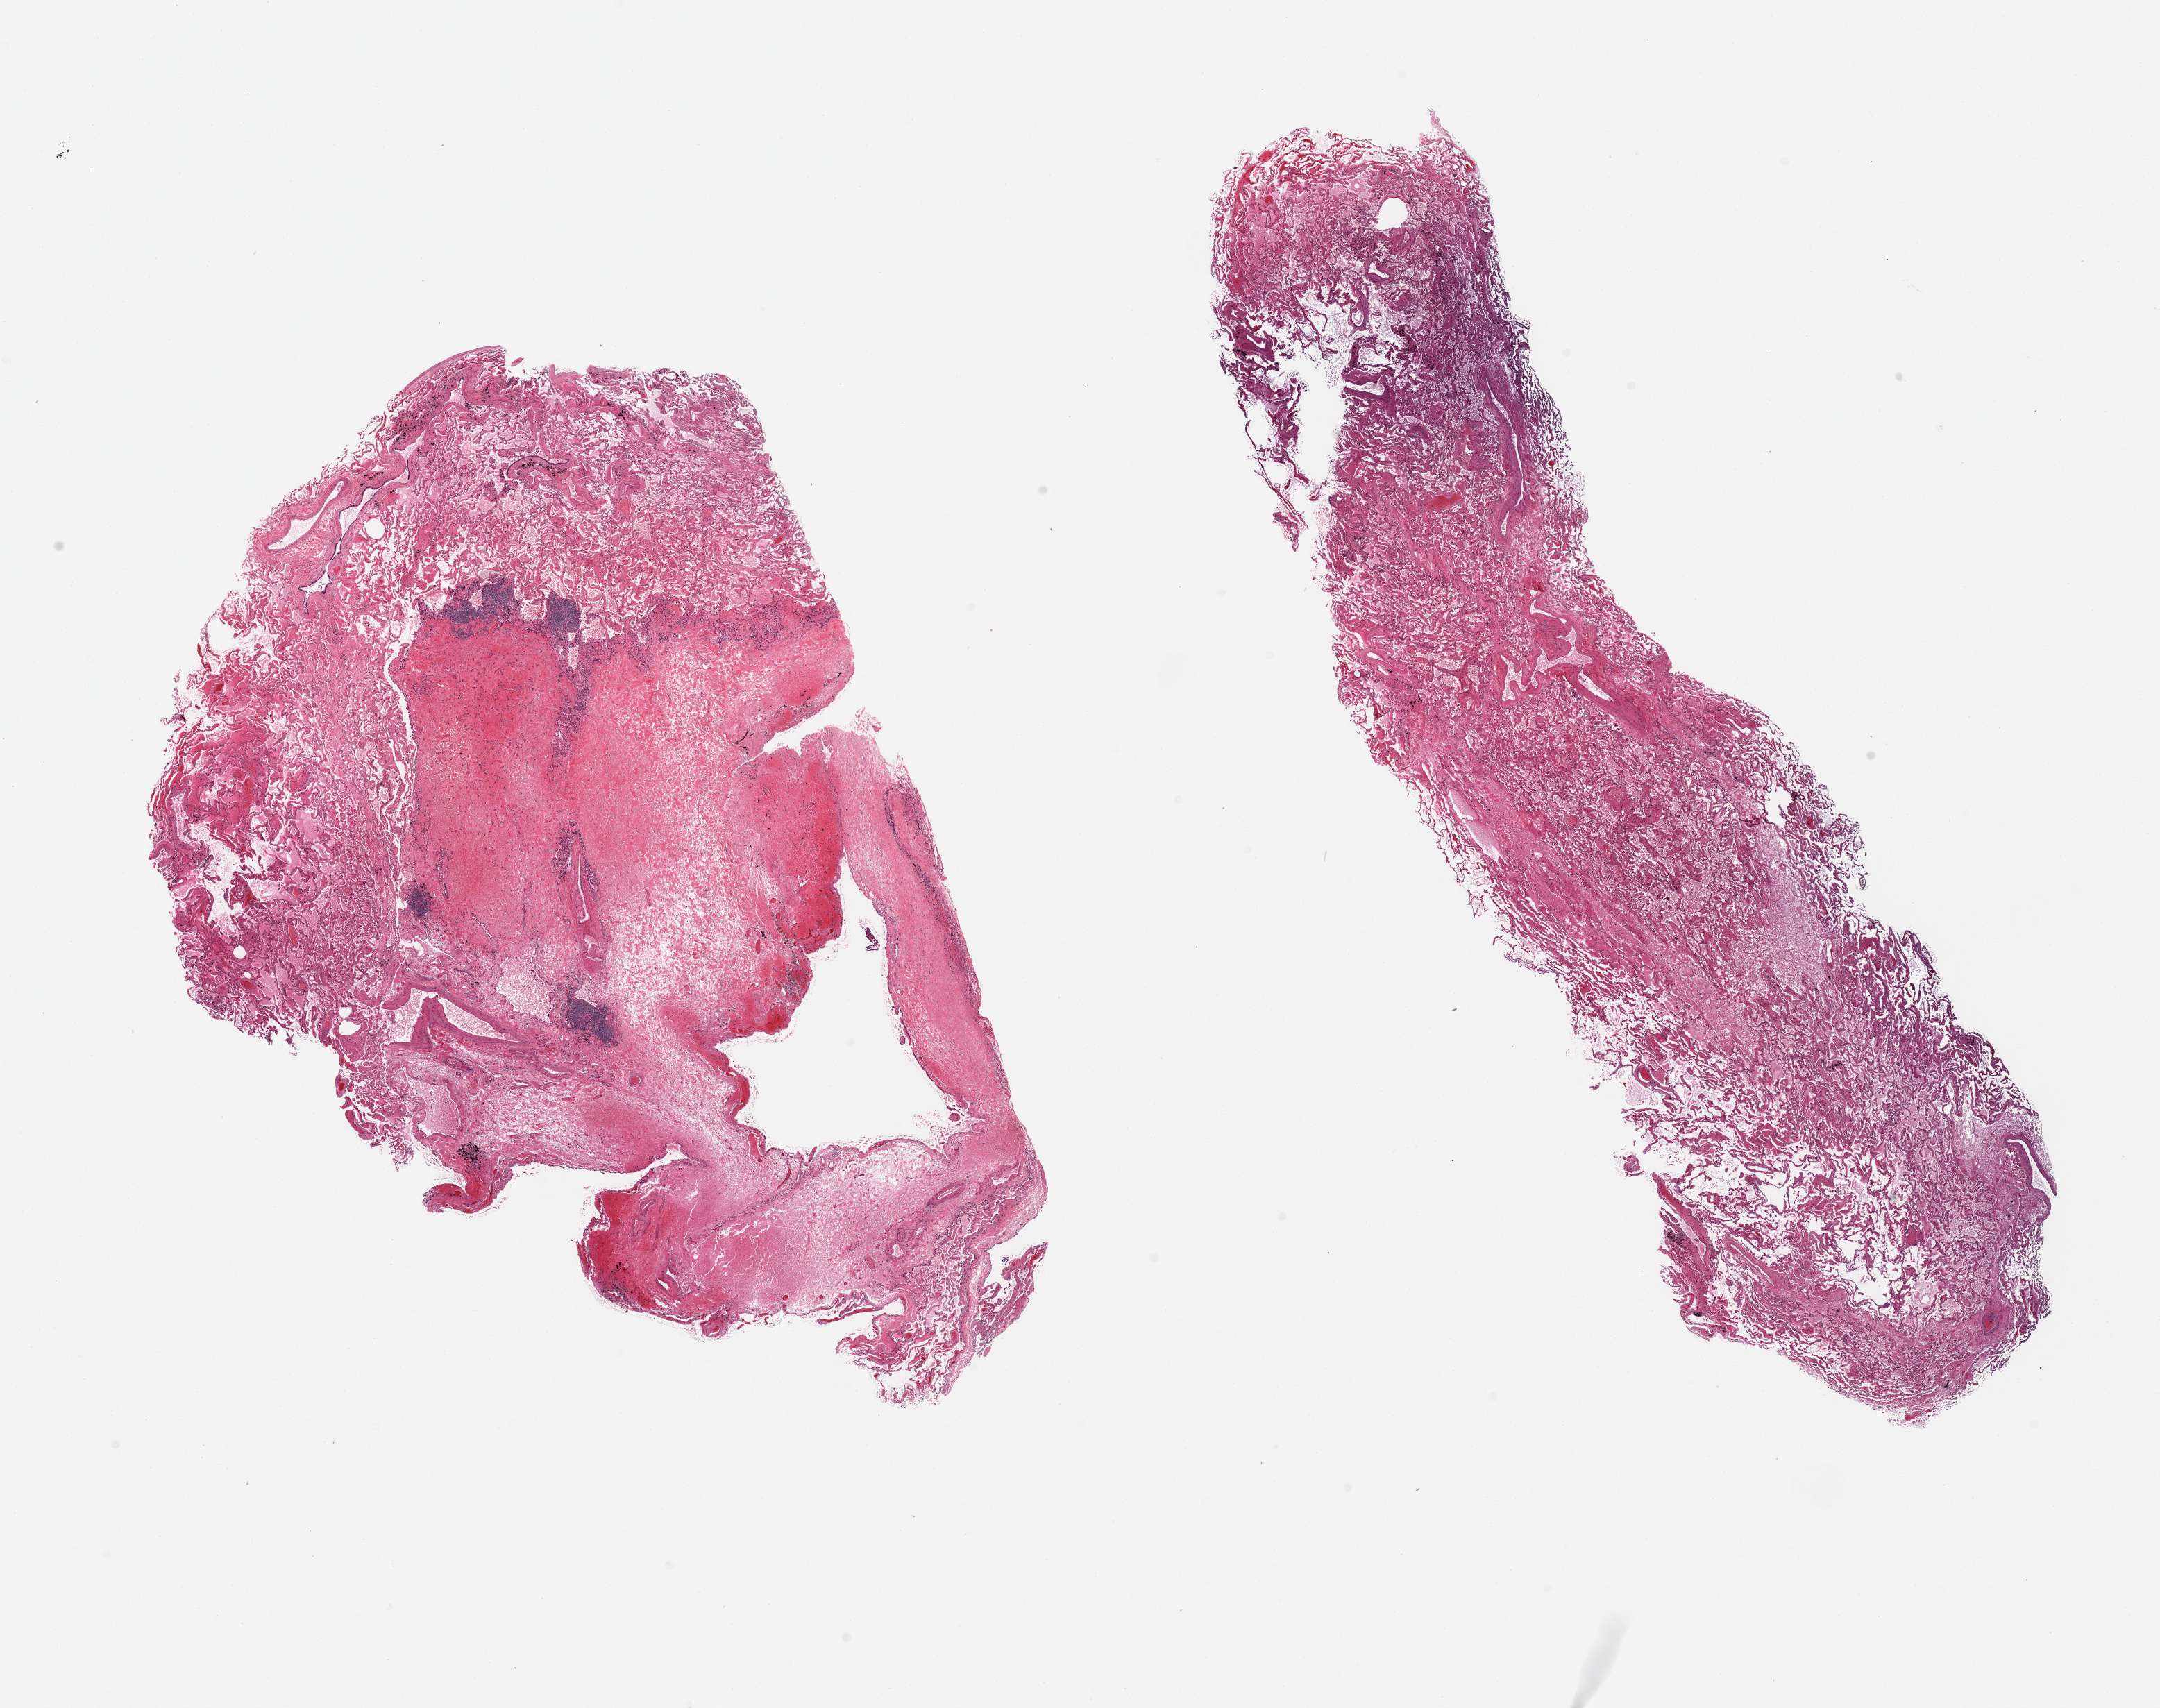
H&E whole-slide image, whole scanned area (about 24.6 x 19.5 mm, acquisition: 20x scan) shown as a low-resolution overview; PAXgene-fixed, paraffin-embedded tissue; target tissue: lung; donor tissue sample. Female donor.
• reviewer comment on this tissue sample: 2 pieces; congestion and edema with hemorrhage/necrosis involving 75% of one tissue fragment bordered by patchy lymphocytic aggregates, rare multinucleated giant cell and hemosiderin-laden macrophages seen